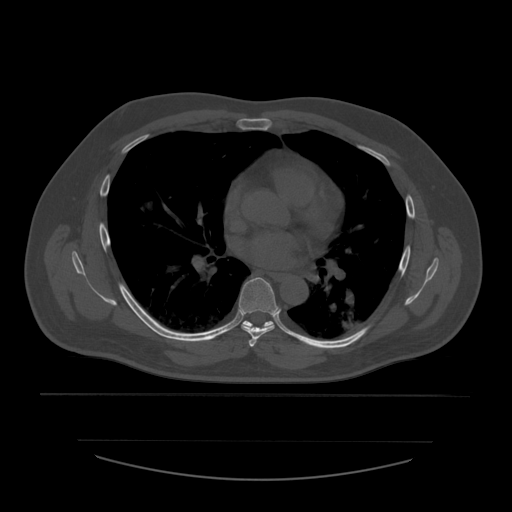
CT including the spine, one axial slice; position 373 of 532 along the scan axis; reconstruction kernel STANDARD; 120 kVp; bone window (W 1800 / L 400 HU); 512 × 512 image matrix, field of view 441 × 441 mm. Patient age 44 years. From the clinical record (not read from this slice): primary cancer: soft tissue sarcoma.
Annotated regions visible in this slice (semi-automatic segmentation, software-assisted and operator-edited):
- T5 vertebra: bounding box [x1, y1, x2, y2] px = [249, 338, 257, 347]
- T6 vertebra: [239, 278, 280, 340]
- T7 vertebra: [243, 321, 275, 327]